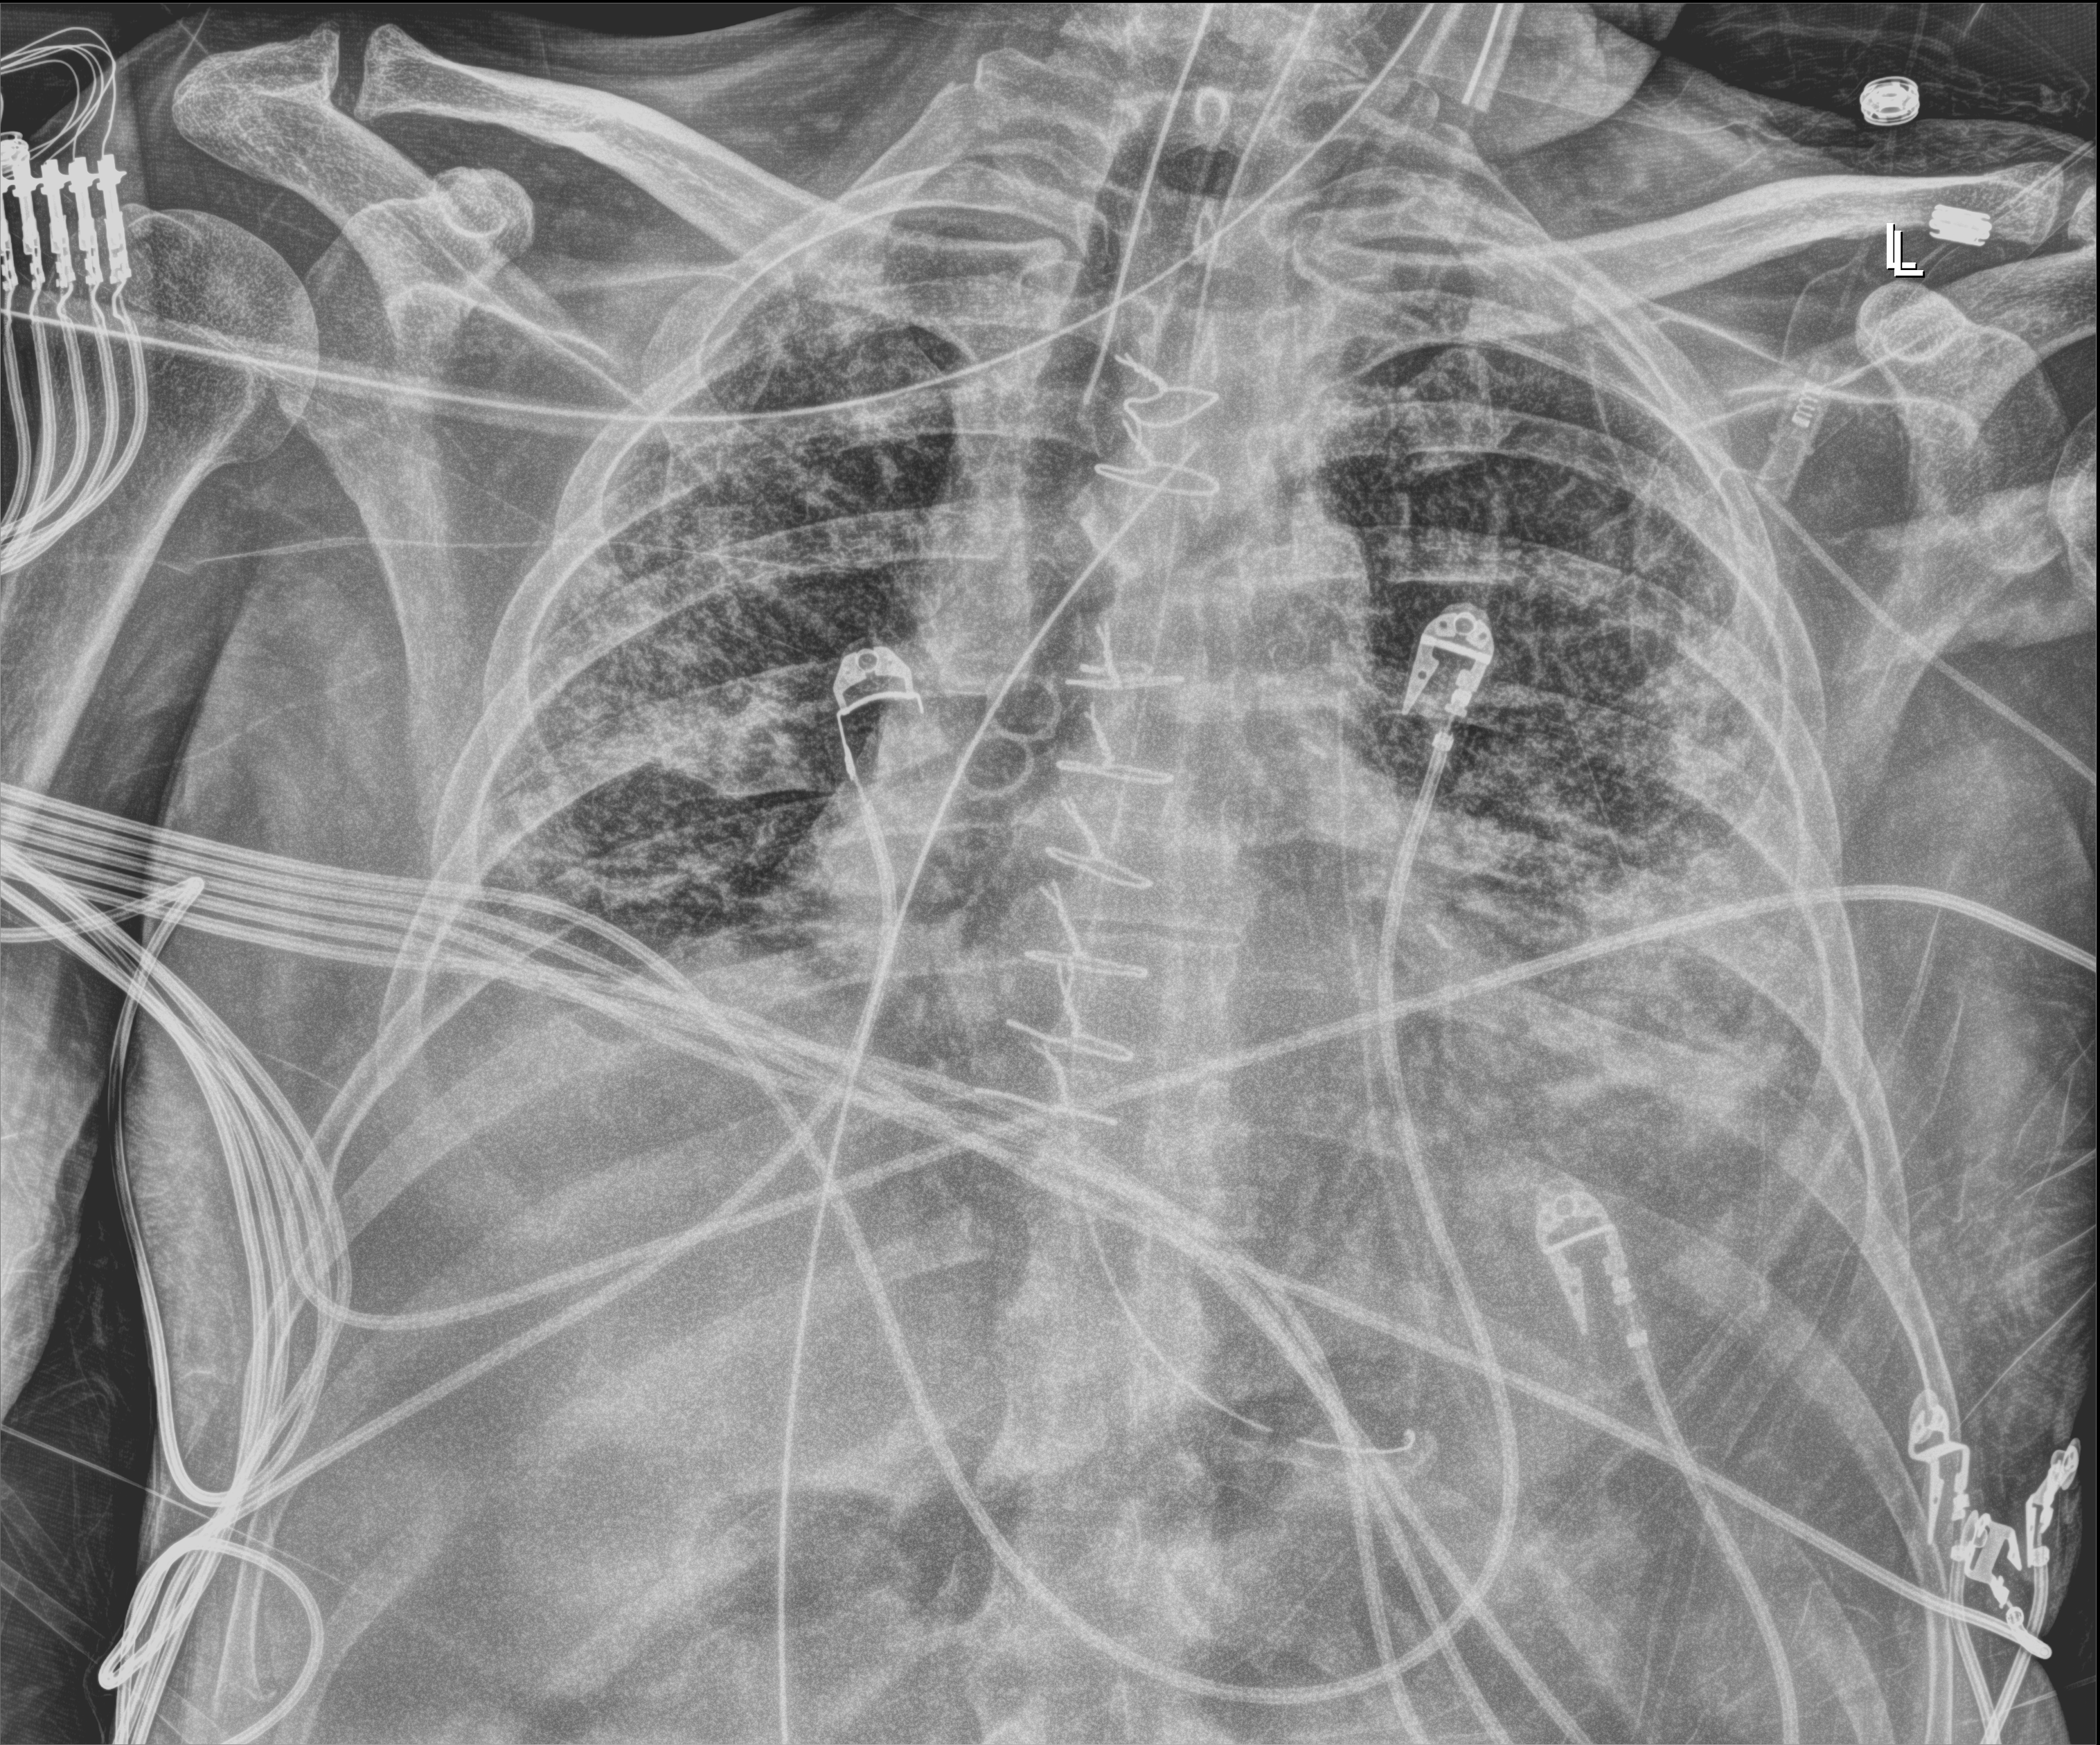
Chest X-ray (portable), anteroposterior (AP) projection. Patient hospitalised with COVID-19; male, aged 18–59 years.
Admission-level facts for this patient (not findings on this image; timing relative to this image not recorded): diabetes (admission record): yes.